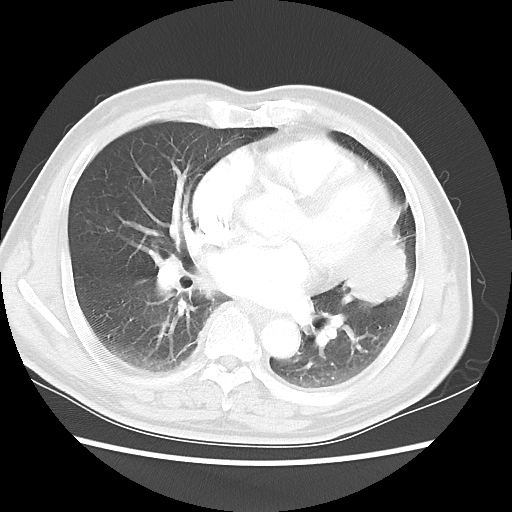
Chest CT, one axial slice. Position 22 of 50 along the scan axis. 120 kVp. Lung window (W 1500 / L -600 HU). 512 × 512 image matrix, field of view 360 × 360 mm. Patient: male, 69 years. Case-level facts recorded for this patient, not image findings: clinical TNM (as recorded): T3 N1 M1a.
Outlined on this slice (bounding box drawn by a radiologist):
- lung tumour (recorded histology: squamous cell carcinoma): bounding box (x1, y1, x2, y2) in pixels: (334, 221, 416, 314)